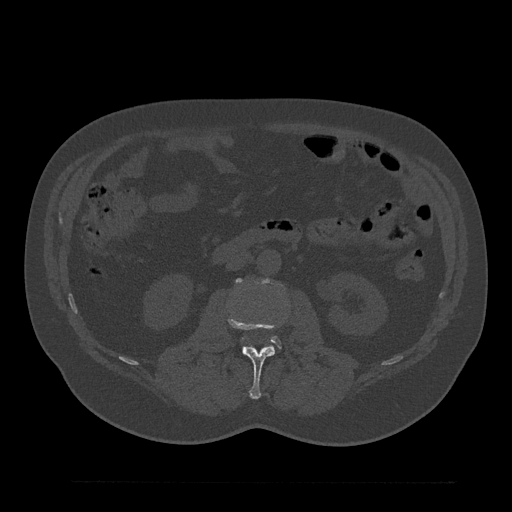
CT including the spine, one axial slice. Position 77 of 797 along the scan axis. Bone window (W 1800 / L 400 HU). 512 × 512 image matrix. Patient: male, 61 years. From the clinical record (not read from this slice): primary cancer: prostate.
Outlined on this slice (semi-automatically segmented with operator editing):
- L2 vertebra: box from (x=228, y=314) to (x=285, y=399) px
- L3 vertebra: (x=237, y=279)–(x=280, y=346)